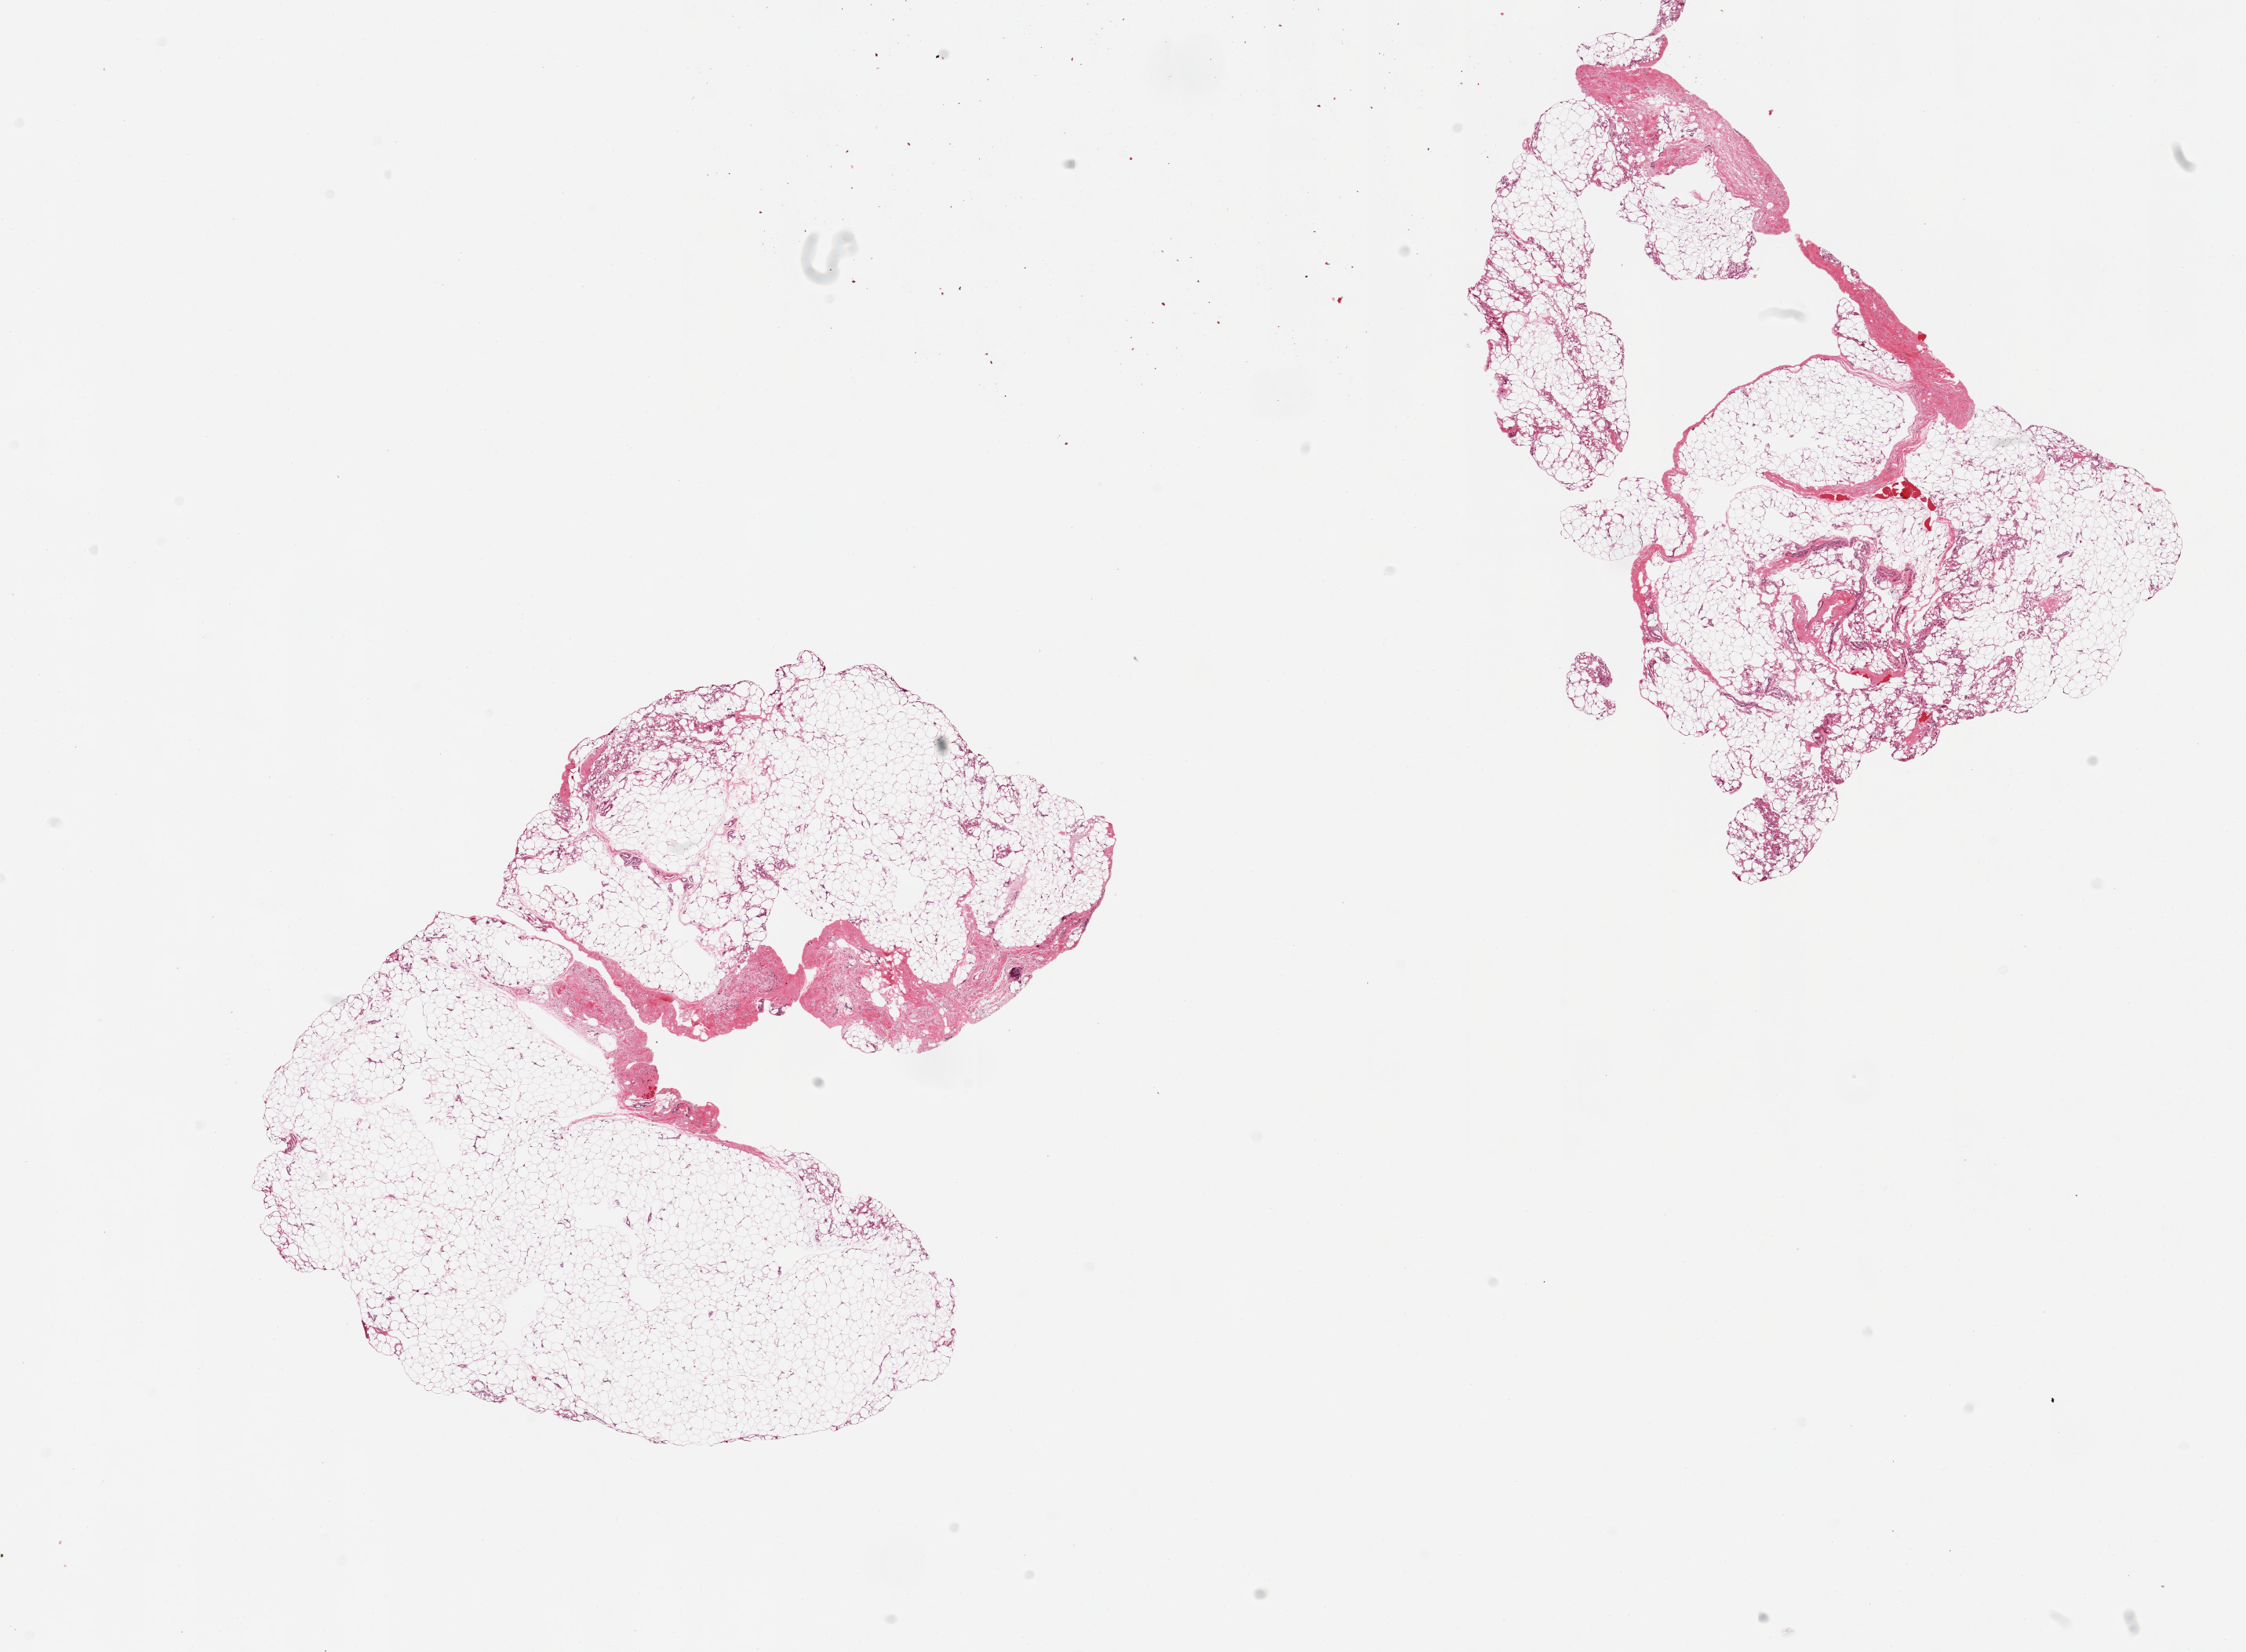
Digitized H&E-stained section, low-resolution overview of the scanned area, about 22.6 x 16.7 mm, PAXgene-fixed, paraffin-embedded tissue, section of adipose tissue (target tissue), tissue donor sample. Donor: female.
Reviewer comment on this tissue sample: 2 pieces; ~10% is fibrous, few foci of skeletal muscle.